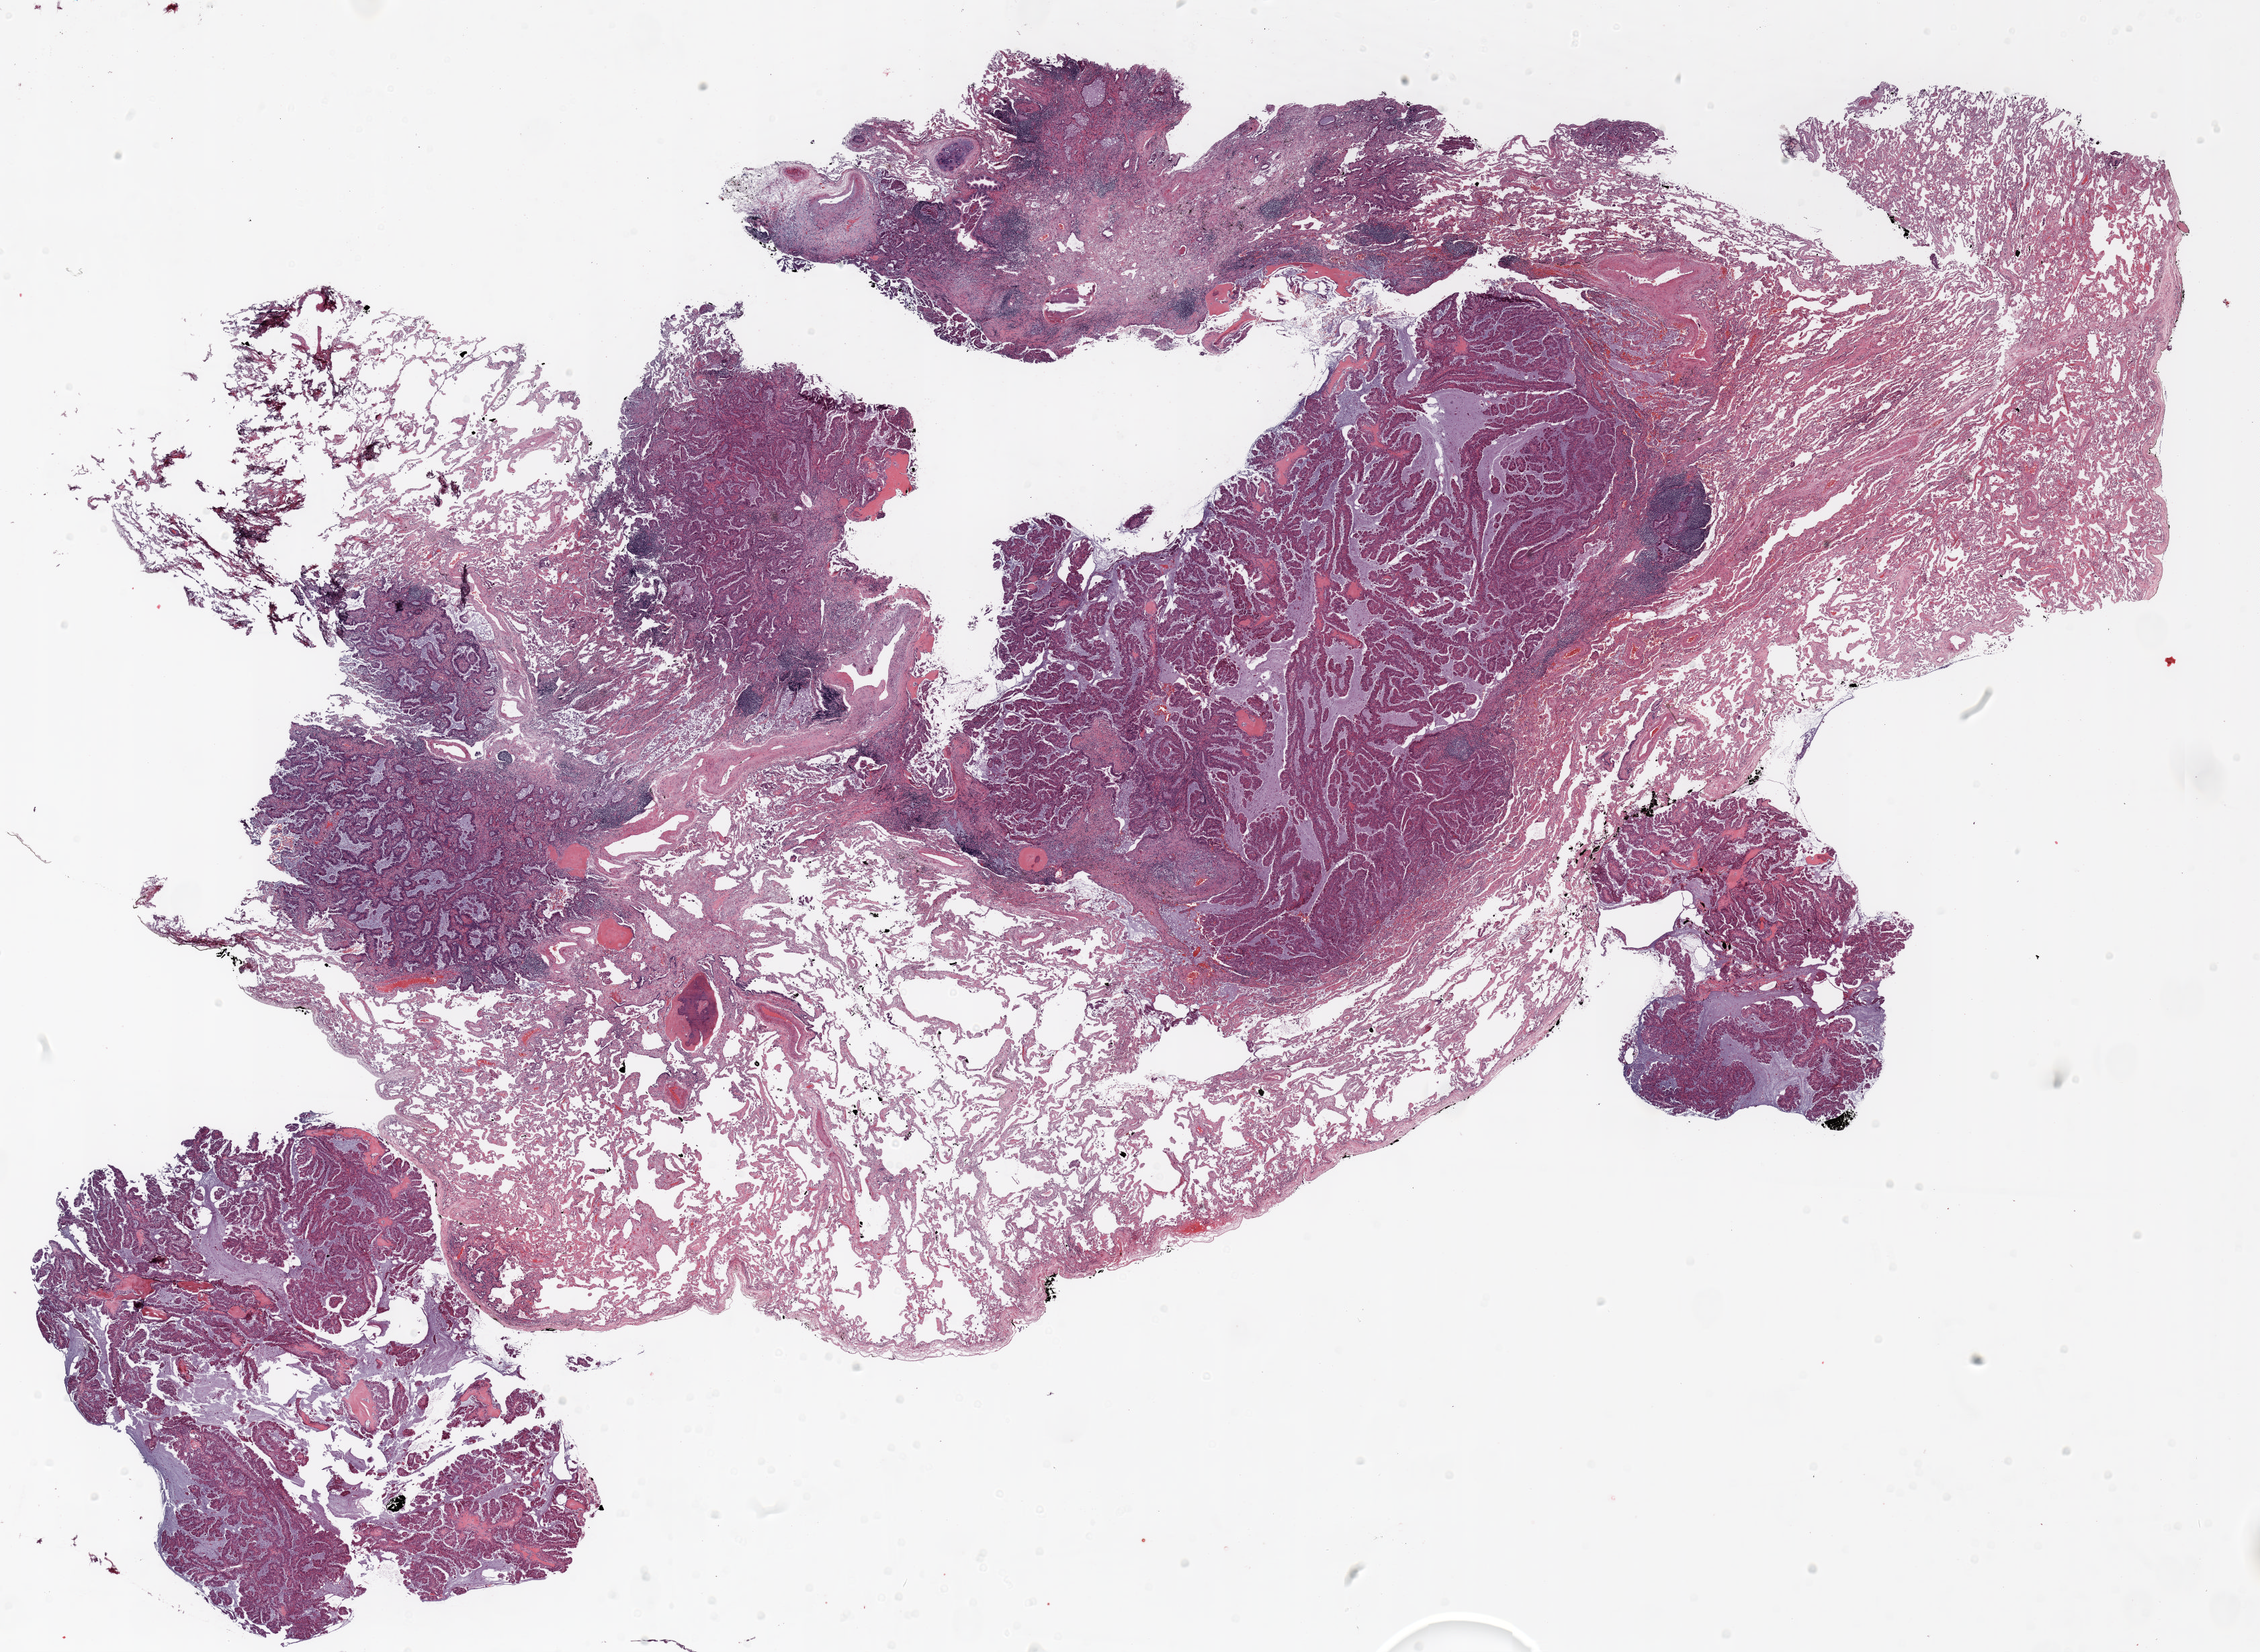
Whole-slide histology image, Hematoxylin and eosin (H&E) stained — whole scanned area (about 27.0 x 19.8 mm, acquisition: 20x scan) shown as a low-resolution overview; formalin-fixed paraffin-embedded (FFPE) section; lung. Female patient, aged 69 at enrolment. Grade: moderately differentiated (G2).
- ICD-O-3 topography: lower lobe of lung (C34.3)
- stage (AJCC 6th edition): IA
- participant's lung-cancer diagnosis: Adenocarcinoma, NOS
- primary tumour location (clinical record): right lower lobe
- tumour size (pathology): 16 mm